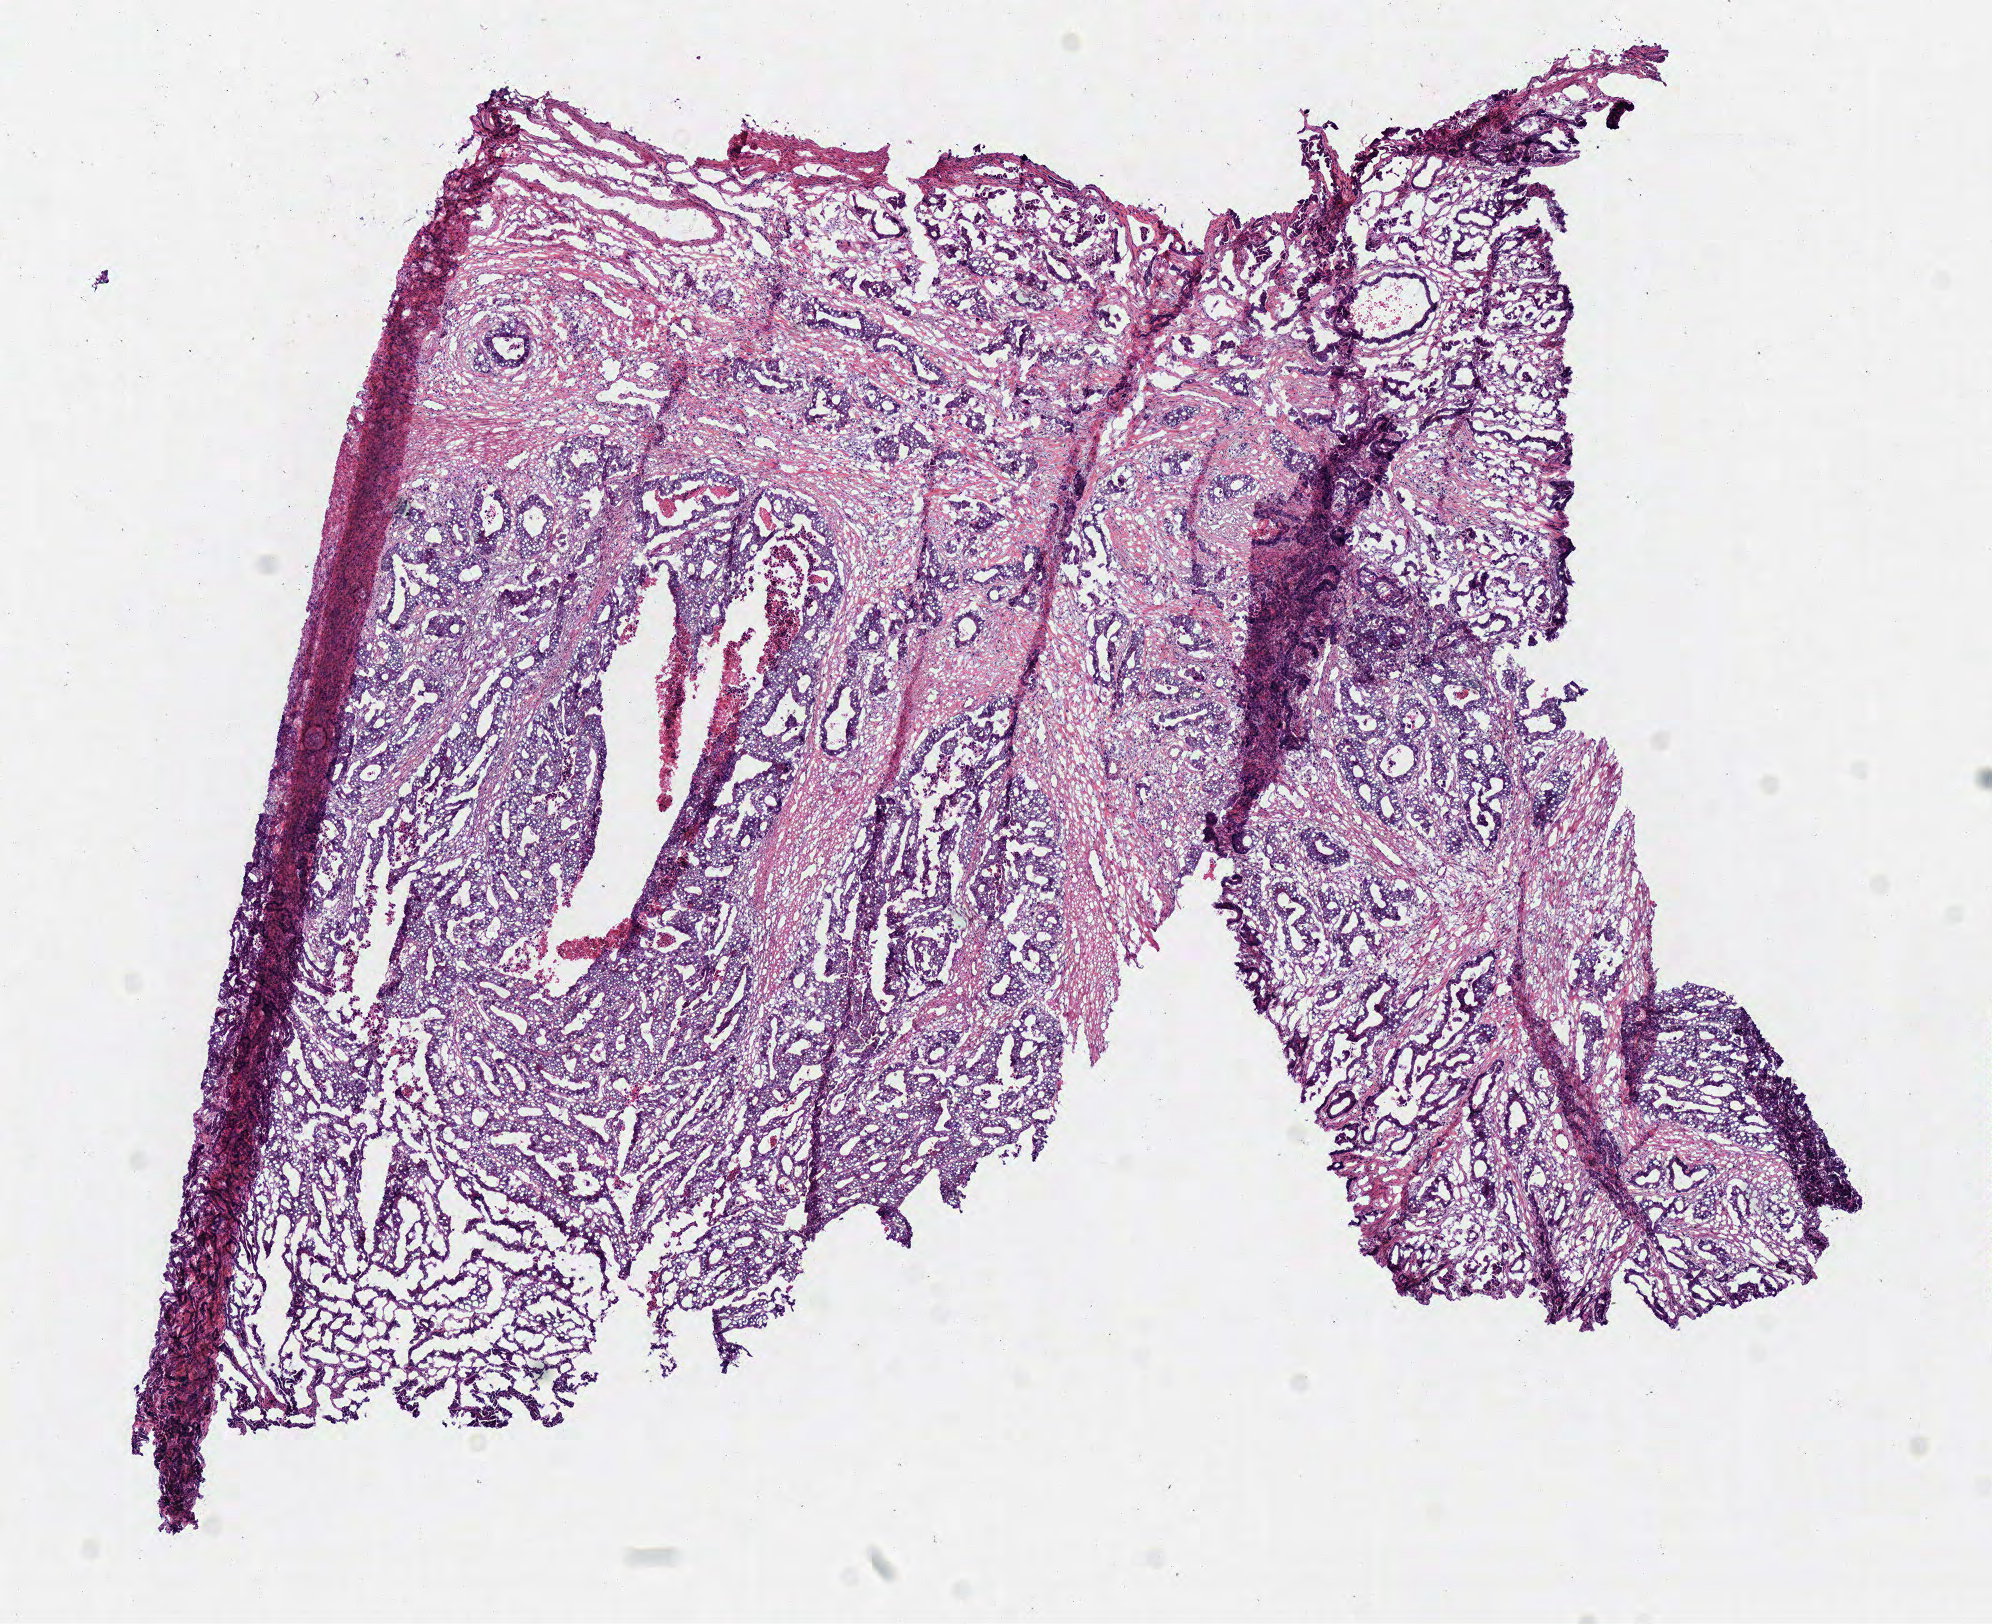
Hematoxylin and eosin (H&E) stained whole-slide image, shown as a low-resolution overview of the whole scanned area (about 7.8 x 6.4 mm, slide scanned at 40x), frozen section from the bottom of the tissue portion, sample: primary tumour, colon. Male patient; age at initial diagnosis 69 years. Pathologist review of this section (percent, as recorded): tumour cells 79%, tumour nuclei 85%, normal cells 1%, stromal cells 10%, necrosis 10%.
AJCC pathologic stage: IIIB. Pathologic diagnosis: Adenocarcinoma, NOS. Lymph nodes positive (case pathology): 1 of 66 examined.